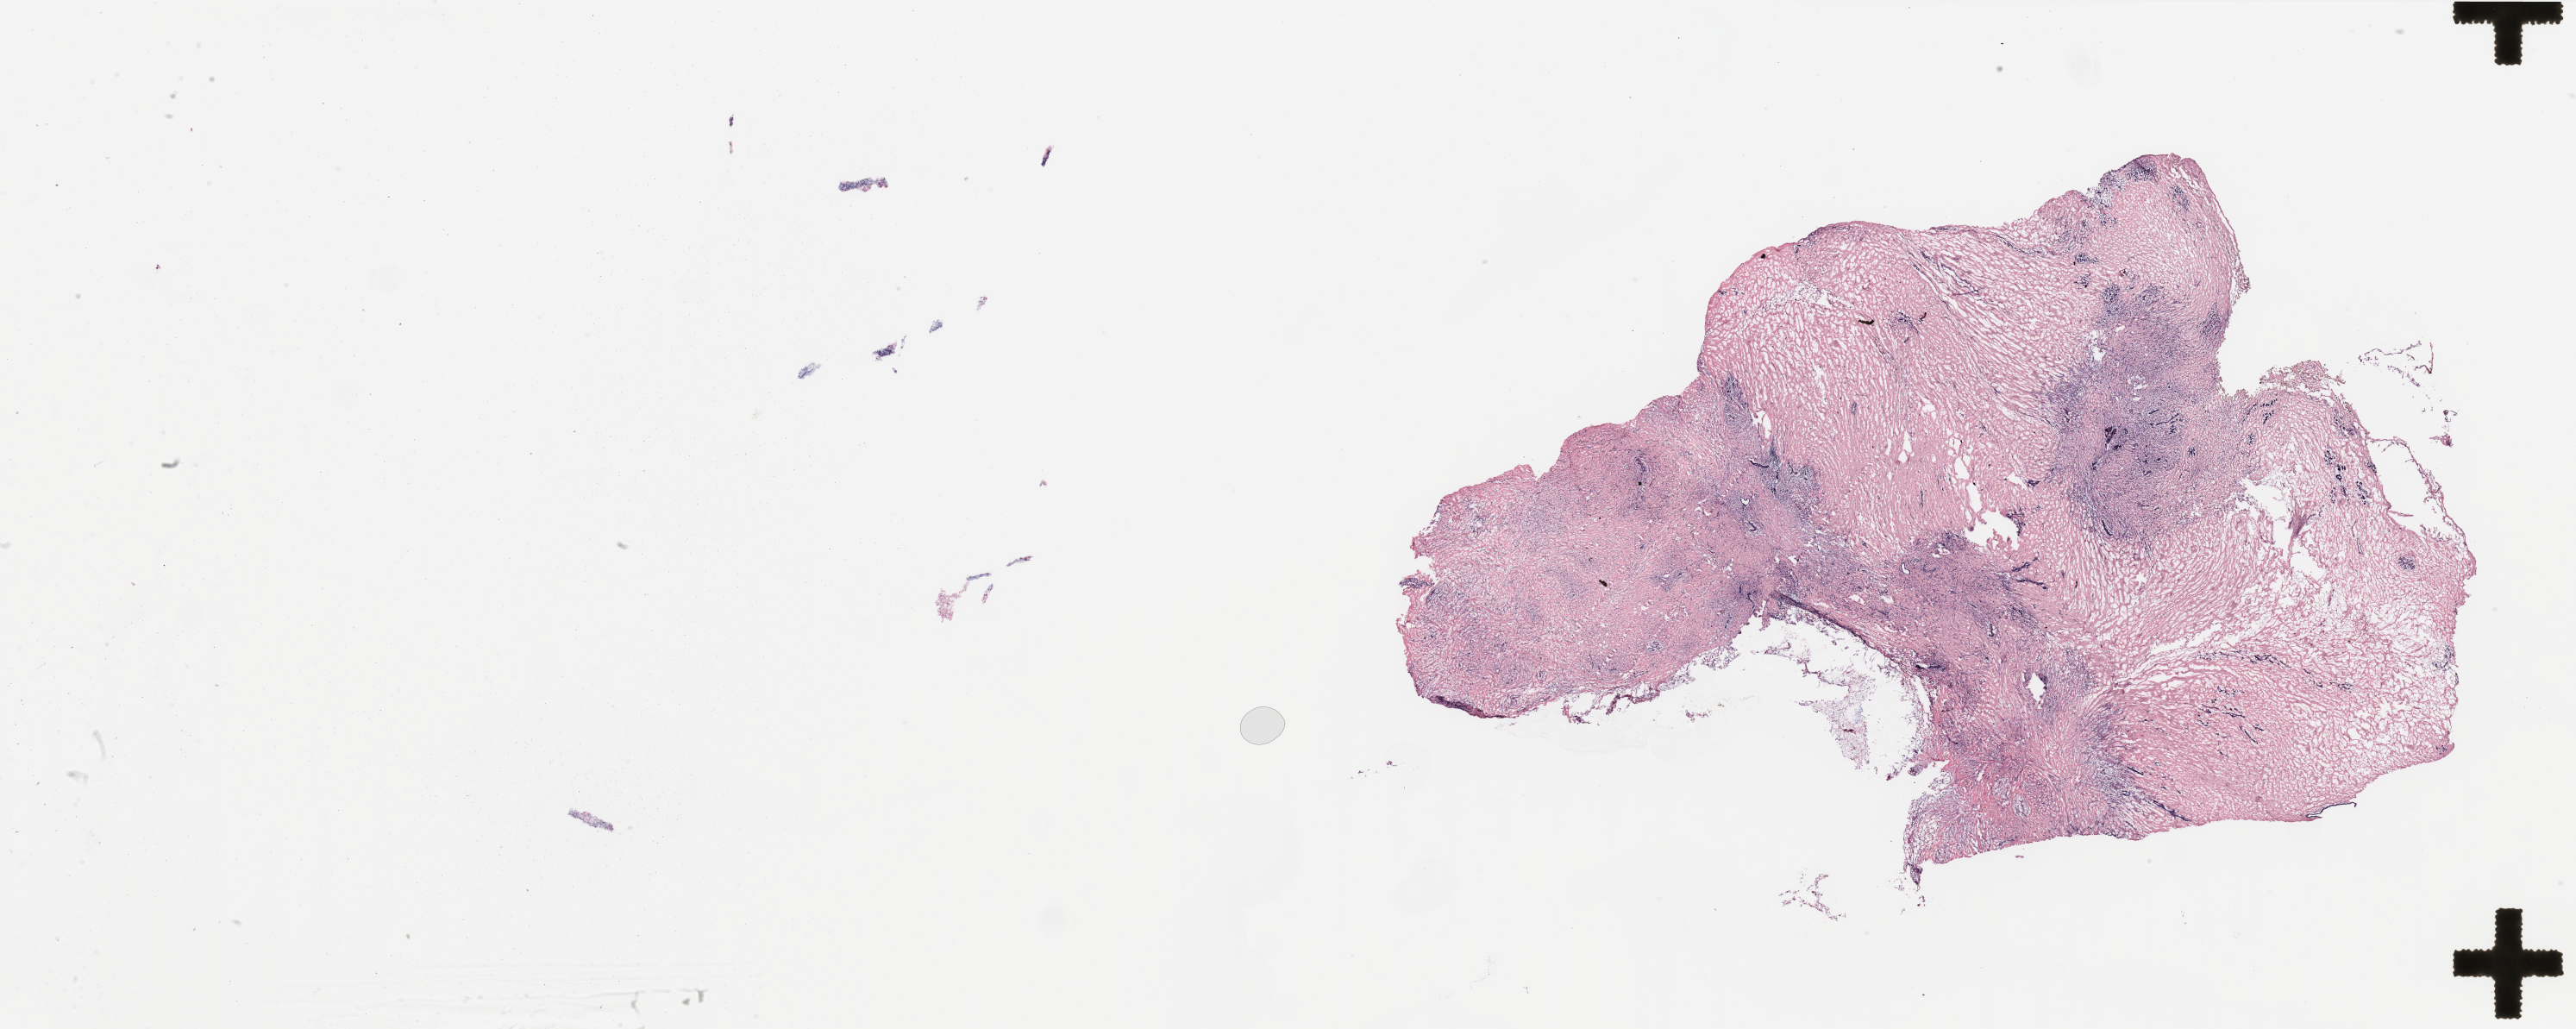
Digitized Hematoxylin and eosin (H&E) stained tissue section (whole slide) — a low-resolution overview of the entire scanned area, about 47.3 x 18.9 mm (slide scanned at 20x). Breast, tissue type not recorded.
• patient diagnosis (cohort enrolment): breast cancer (breast)